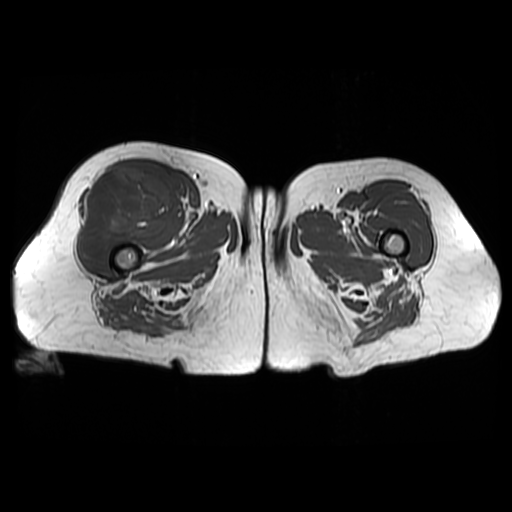
MRI of an extremity soft-tissue mass, one axial slice. Slice 34 of 48 in the series (ordered by position). 512 × 512 image matrix. Female patient. Case-level facts recorded for this patient, not image findings: histological type: pleiomorphic undifferentiated sarcoma; grade: high; site of the primary tumour: right quadricep.
Structures marked on this image (expert manual segmentation):
- gross tumour volume including surrounding oedema: bounding box [x1, y1, x2, y2] px = [78, 167, 178, 264]
- gross tumour volume (mass): [78, 167, 178, 264]